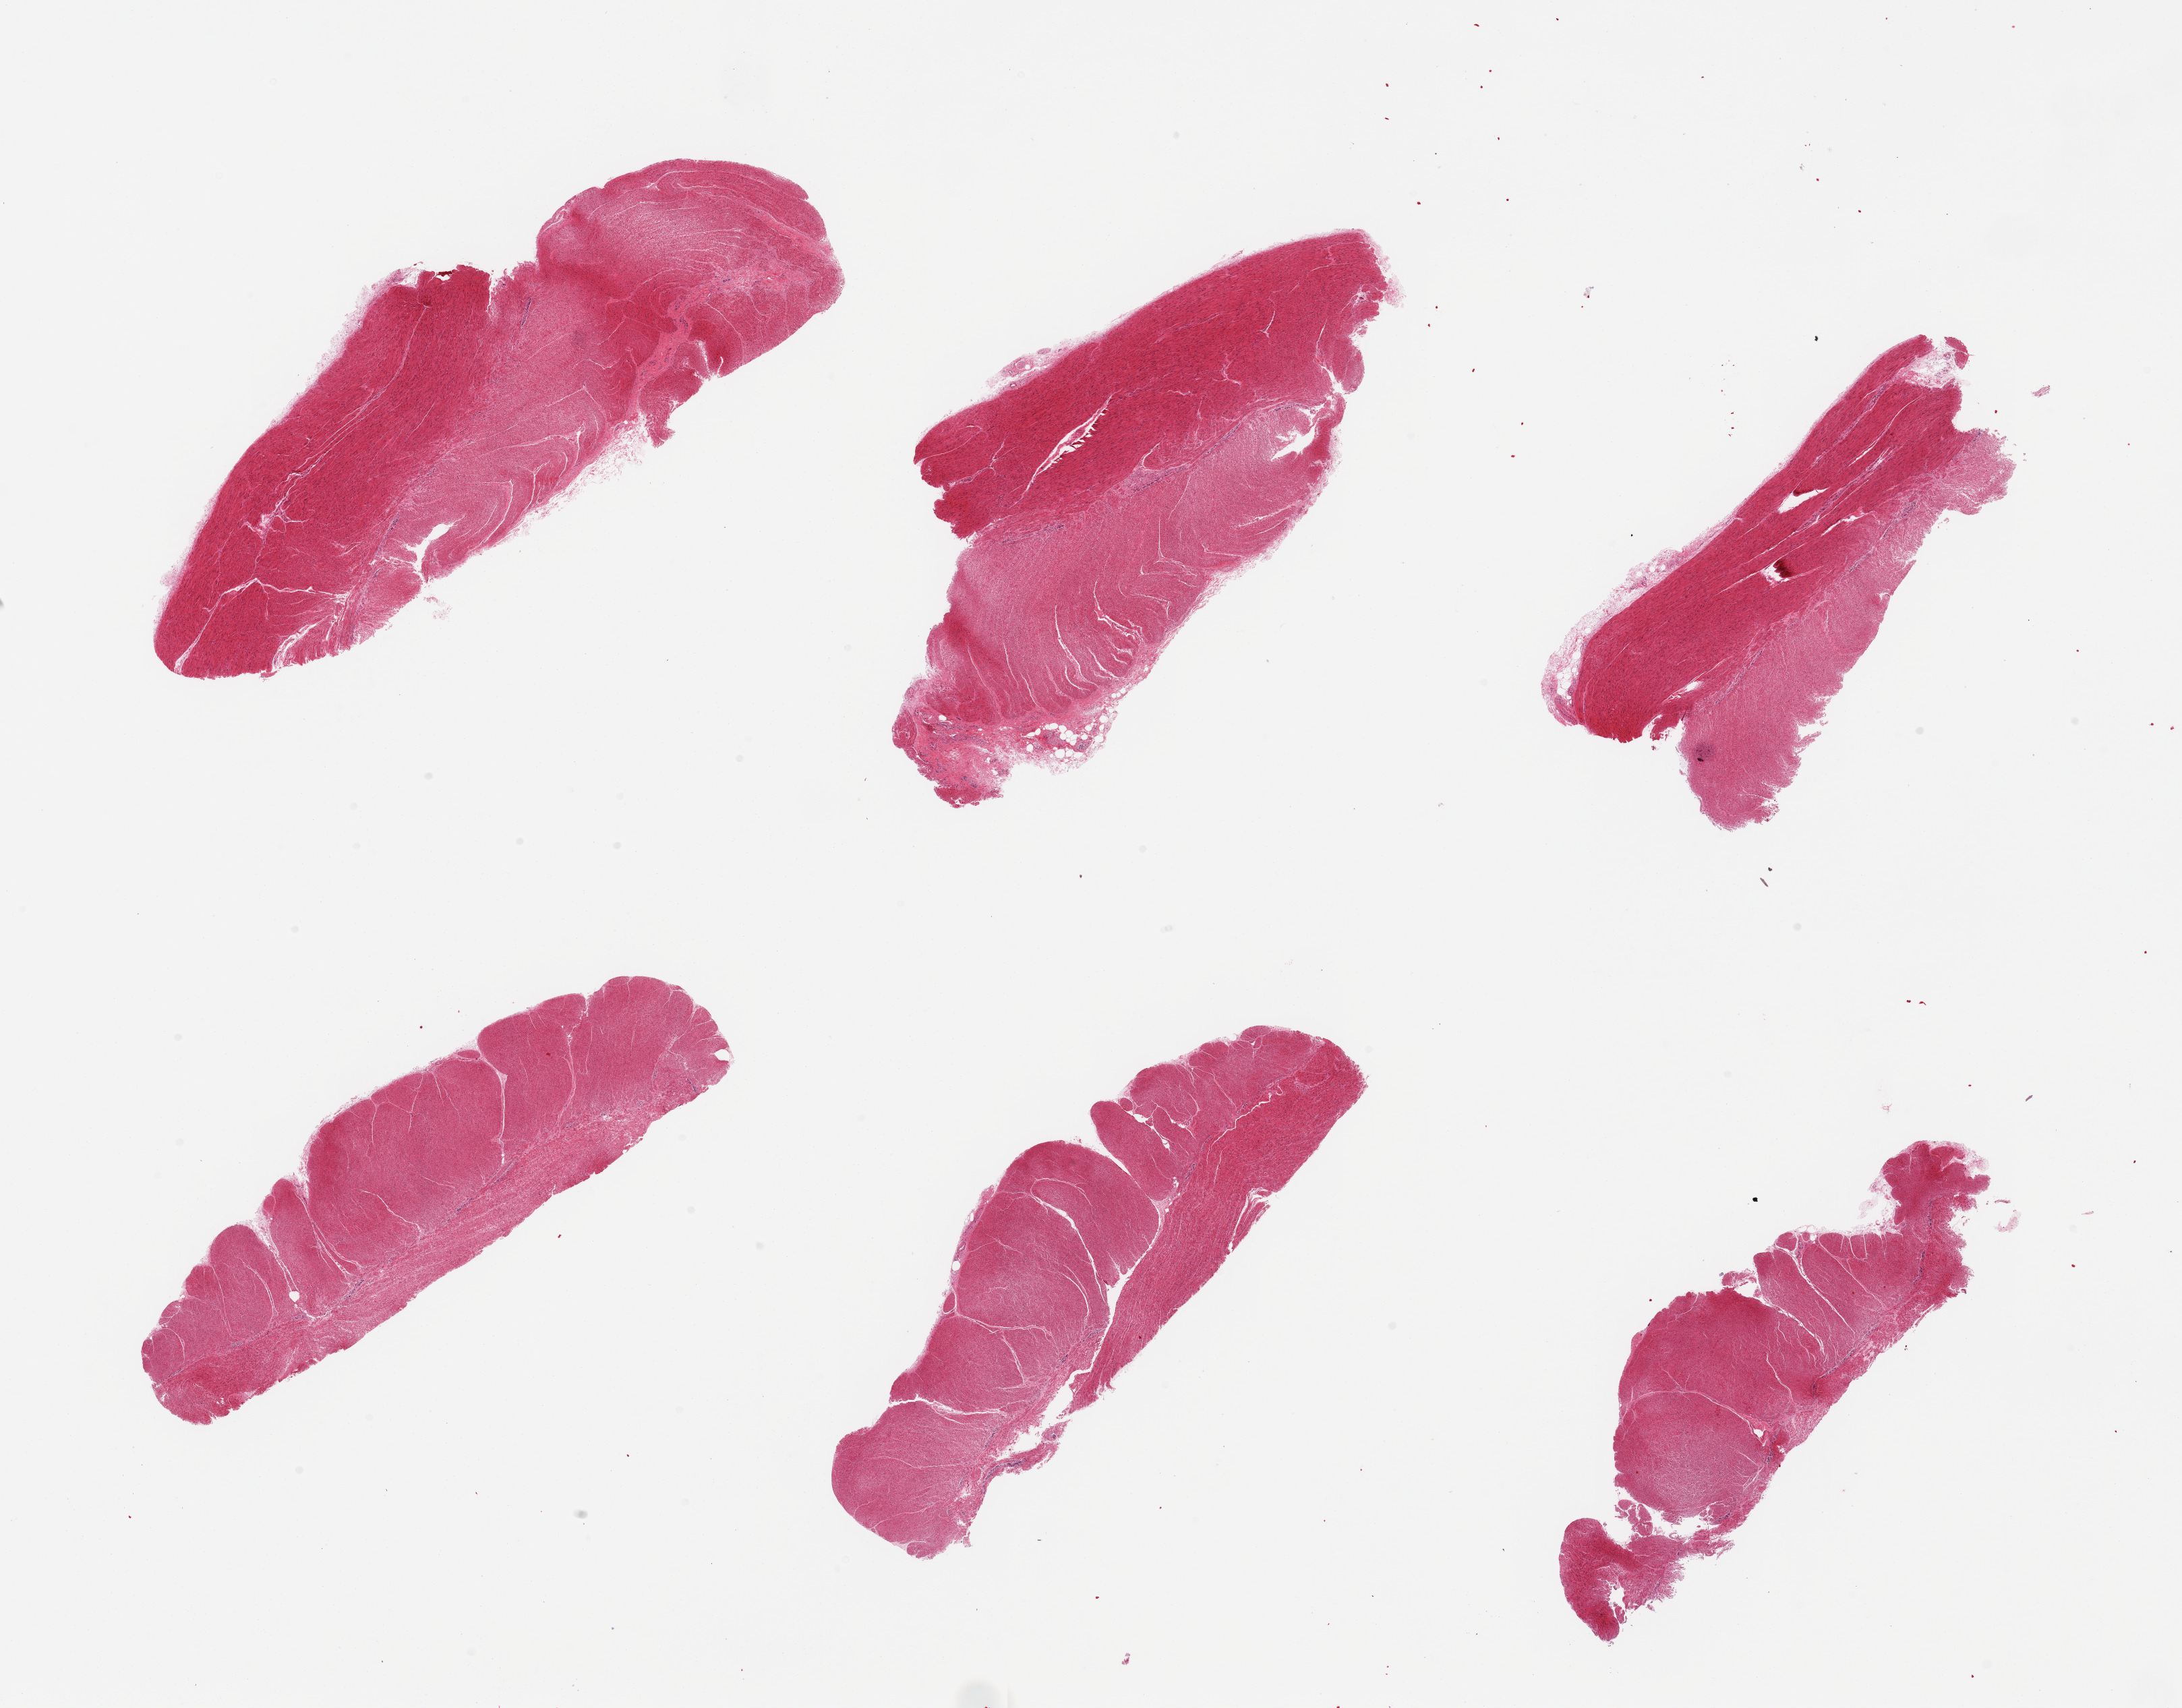
H&E whole-slide image, a low-resolution overview of the entire scanned area, about 25.6 x 20.0 mm, PAXgene-fixed paraffin-embedded (PFPE) section, section of sigmoid colon (target tissue), tissue donor sample. Donor: male.
Pathologist's review note for this sample: 6 pieces; well trimmed.